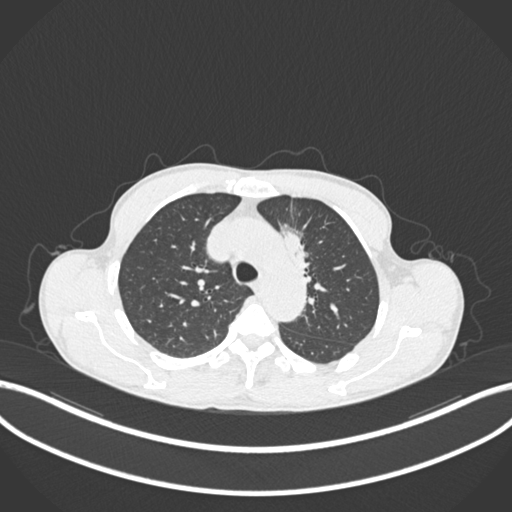
Chest CT, one axial slice. Position 146 of 211 along the scan axis. Reconstruction kernel B30f. 120 kVp. Lung window (W 1500 / L -600 HU). 1 mm slice thickness. 512 × 512 image matrix, field of view 400 × 400 mm. Patient: male, 58 years. Case-level facts recorded for this patient, not image findings: clinical TNM (as recorded): T1c N1 M0.
Annotated regions visible in this slice (rectangle marked by the reading radiologist):
- lung tumour (recorded histology: adenocarcinoma): bounding box (x1, y1, x2, y2) in pixels: (276, 221, 322, 287)